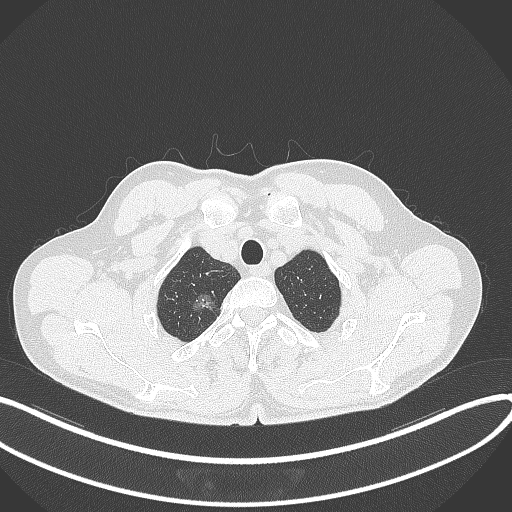
Chest CT, one axial slice. Reconstruction kernel B70f. 120 kVp. Lung window (W 1500 / L -600 HU). 512 × 512 image matrix, field of view 400 × 400 mm. Patient: male, 58 years. Case-level facts recorded for this patient, not image findings: clinical TNM (as recorded): T1c N0 M0.
Annotated regions visible in this slice (bounding box drawn by a radiologist):
- lung tumour (recorded histology: adenocarcinoma): bounding box [x1, y1, x2, y2] px = [190, 293, 229, 321]